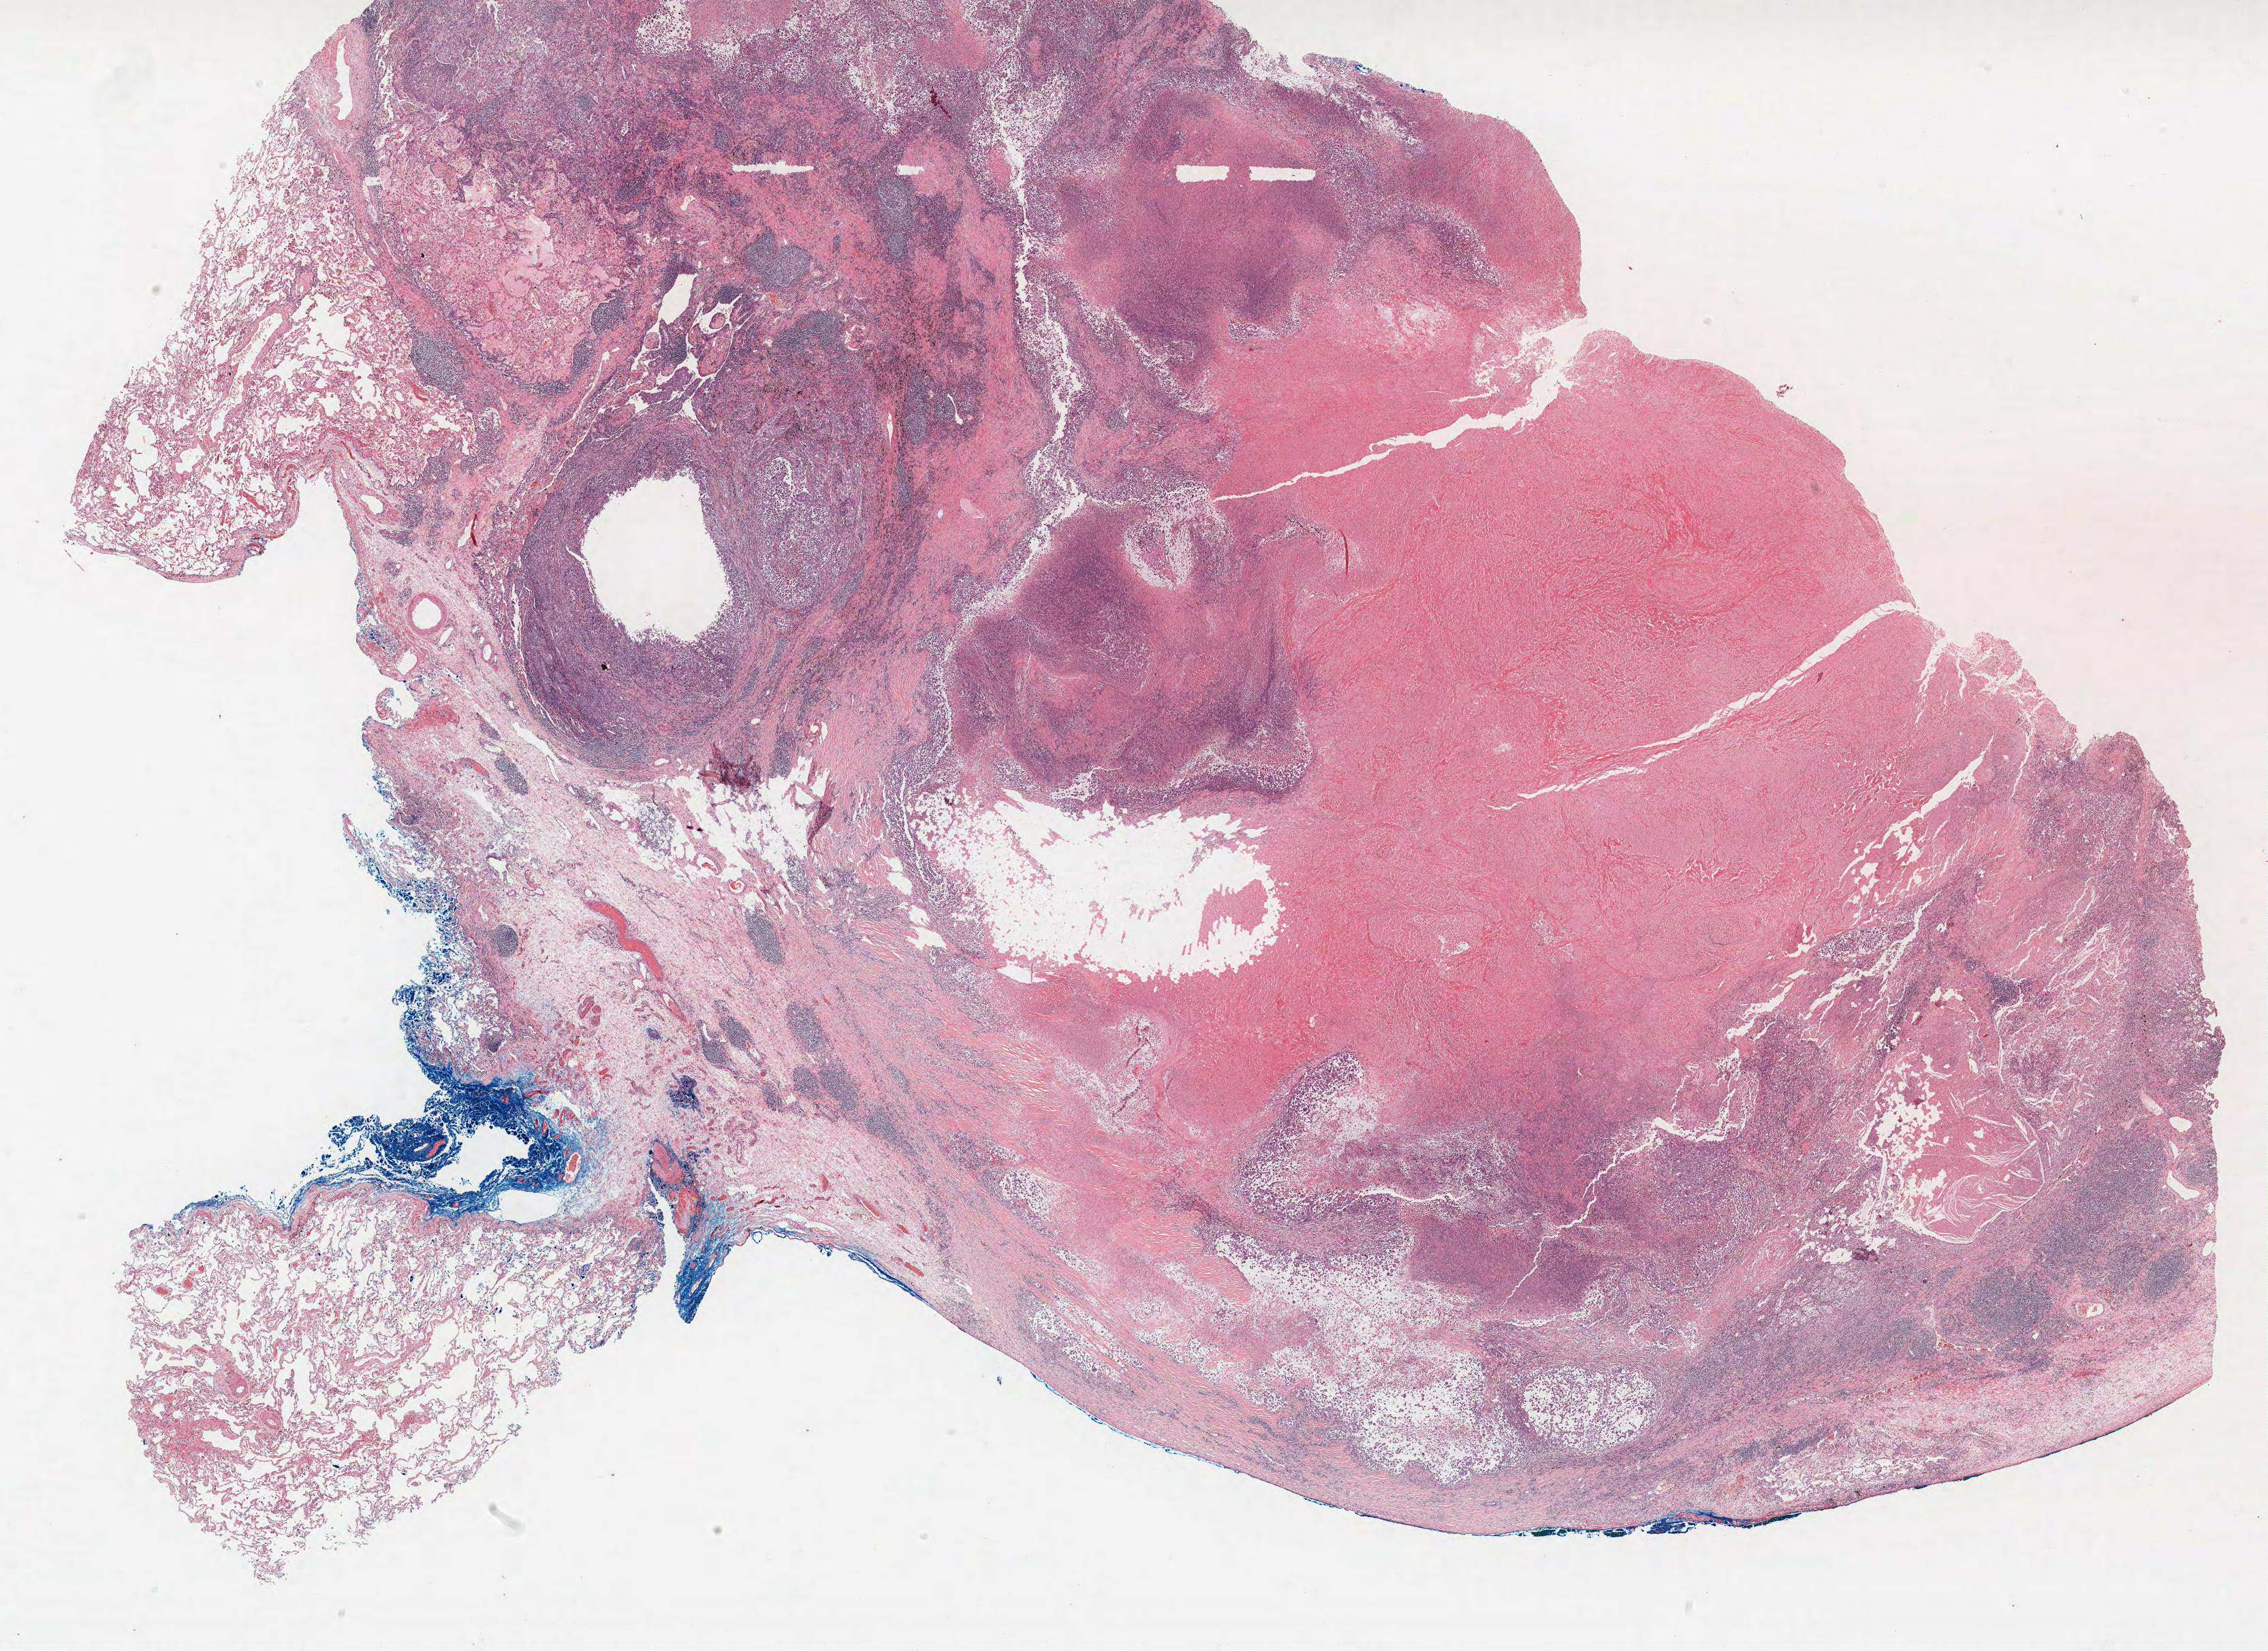
Hematoxylin and eosin (H&E) stained whole-slide image, whole scanned area (about 26.6 x 19.4 mm, acquisition: 40x scan) shown as a low-resolution overview. FFPE section. Lung tissue. Female, age 64 at enrolment. Grade: poorly differentiated (G3).
Primary tumour location (clinical record): left upper lobe, left lower lobe. Tumour size (pathology): 25 mm. Stage (AJCC 6th edition): IV. ICD-O-3 topography: lower lobe of lung (C34.3). Participant's lung-cancer diagnosis: Adenocarcinoma, NOS.